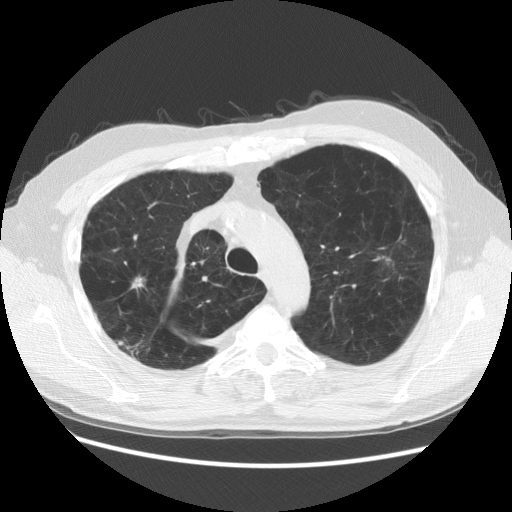
Low-dose screening chest CT, axial slice. Third screening round (two years after baseline). Lung window (W 1500 / L -600 HU). 512 × 512 image matrix, field of view 377 × 377 mm. Male participant, aged 58 years at enrolment. Former smoker at enrolment.
Lesion marked by an expert reader, bounding box [x1, y1, x2, y2] px = [114, 259, 156, 307]. The screening reader recorded 3 non-calcified nodules or masses ≥4 mm on this exam (right lower lobe, right upper lobe, right upper lobe); which of them this box marks is not recorded. Later outcome: lung cancer diagnosed 88 days after this screen — squamous cell carcinoma, NOS, right upper lobe, moderately differentiated (G2), stage IB (AJCC 6th edition), 18 mm at pathology.